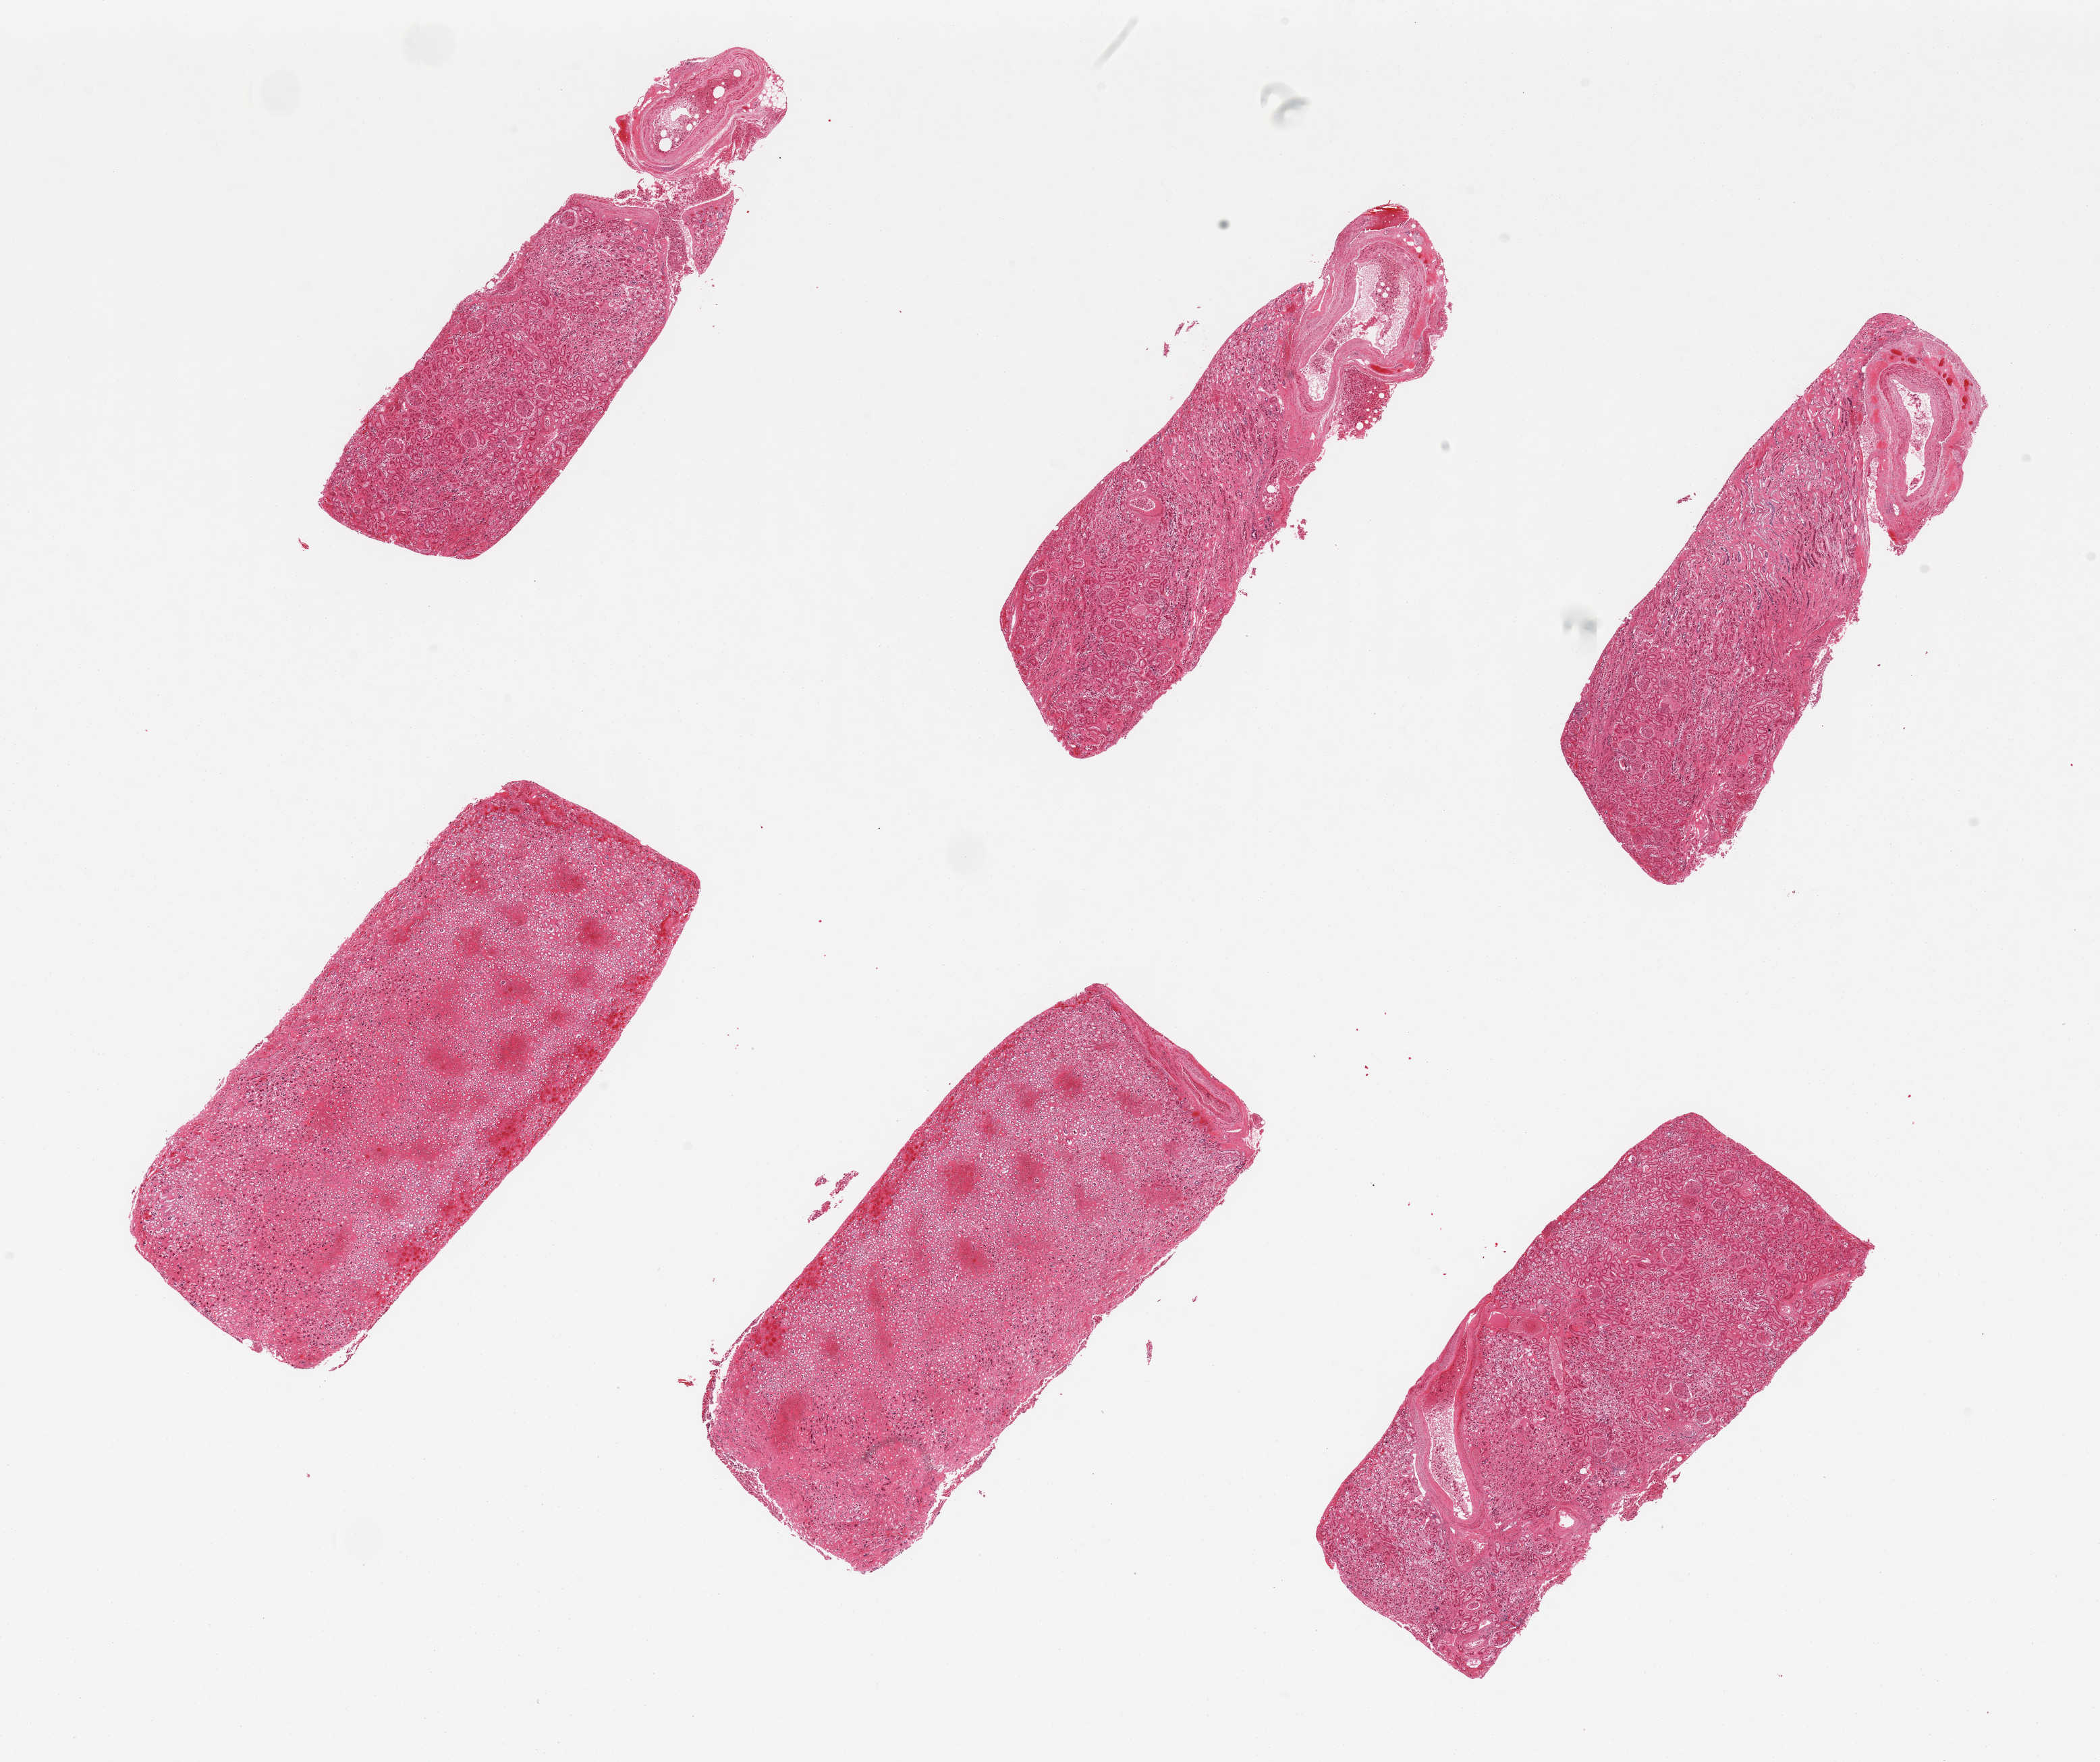
Hematoxylin and eosin (H&E) whole-slide image, brightfield — a low-resolution overview of the entire scanned area, about 24.6 x 20.6 mm (slide scanned at 20x), PAXgene-fixed paraffin-embedded (PFPE) section, section of renal cortex (target tissue), donor tissue sample. Donor: male.
Reviewer comment on this tissue sample: 6 pieces, renal cortex (target) and medulla (not target) with at least moderate autolysis.